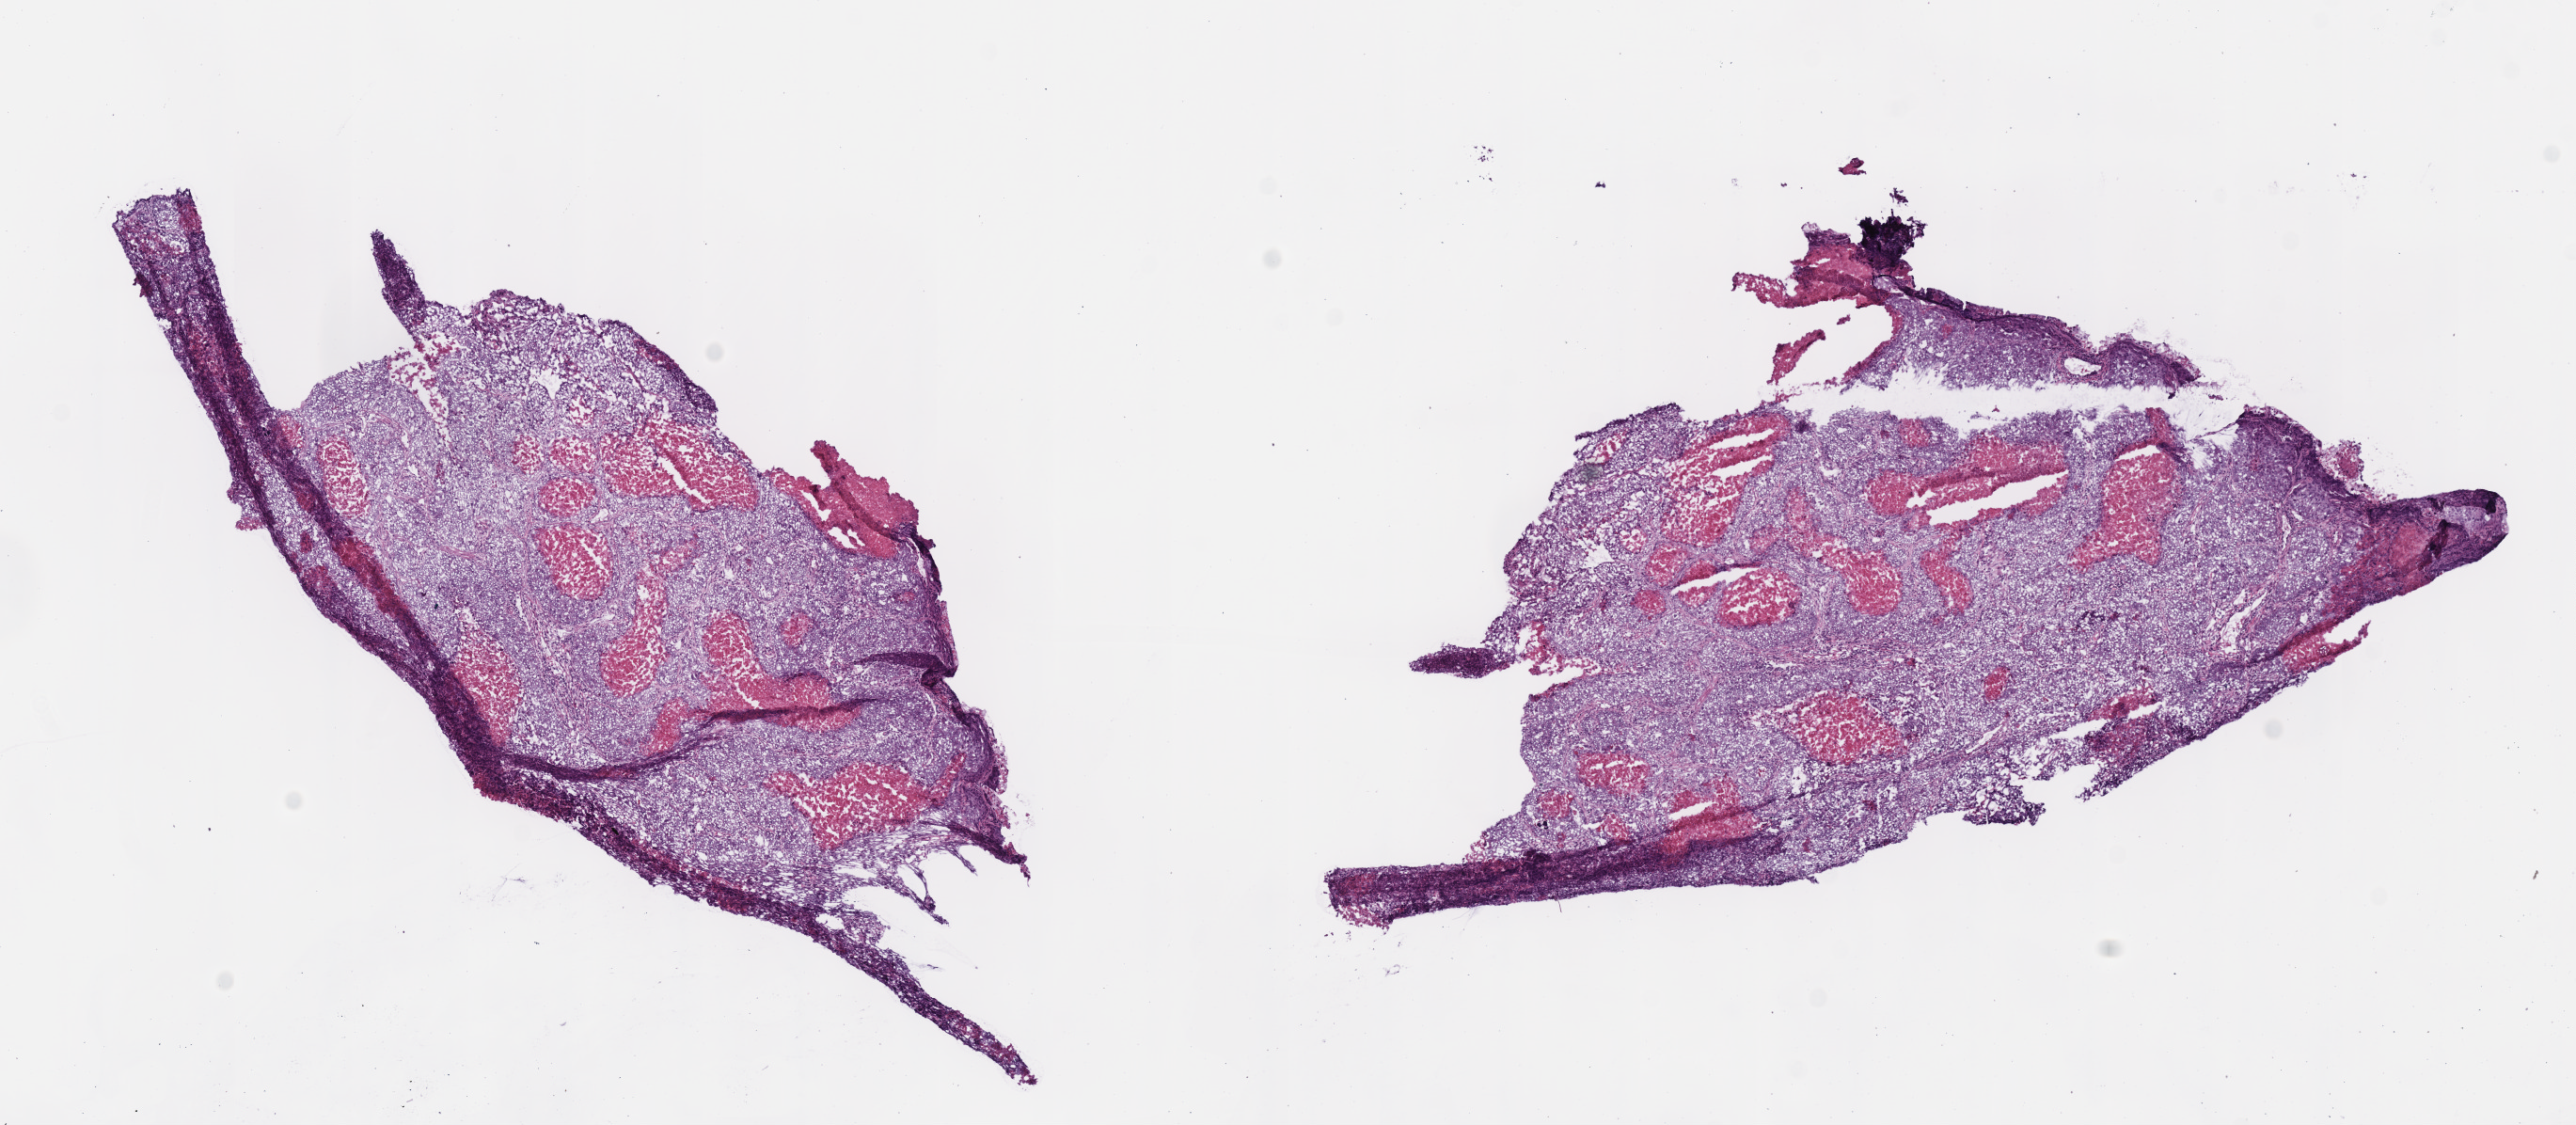
Hematoxylin and eosin (H&E) stained whole-slide image, whole scanned area (about 10.8 x 4.7 mm, slide scanned at 40x) shown as a low-resolution overview, frozen section from the bottom of the tissue portion, sample: primary tumour, lung. Female, age 65 years at initial diagnosis. Slide review estimates, as recorded: tumour cells 82%, tumour nuclei 85%, normal cells 0%, stromal cells 0%, necrosis 18%. Infiltration values recorded for this section: lymphocyte infiltration 3%.
Laterality: left. AJCC pathologic stage: IIIB (6th edition). Diagnosis: Adenocarcinoma with mixed subtypes (lower lobe, lung).